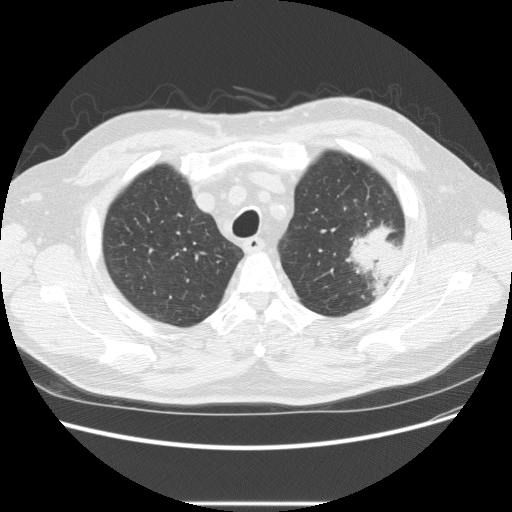
Axial slice from a low-dose chest CT screening exam; first (baseline) screen; lung window (W 1500 / L -600 HU); 2.5 mm slice thickness. Male, age 73 years at enrolment. Former smoker at enrolment.
Lesion marked by an expert reader, box from (x=332, y=216) to (x=410, y=284) px. The screening reader recorded 2 non-calcified nodules or masses ≥4 mm on this exam (left upper lobe, right upper lobe); which of them this box marks is not recorded. Lung cancer was diagnosed 11 days after this screen: bronchiolo-alveolar adenocarcinoma, NOS, other location, well differentiated (G1), stage IV (AJCC 6th edition).